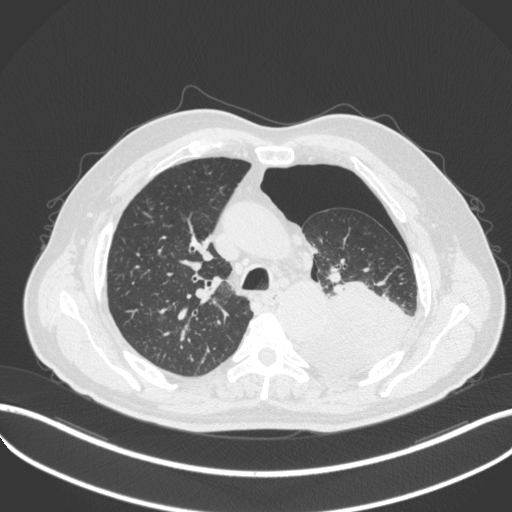
Chest CT, one axial slice. Position 357 of 466 along the scan axis. 120 kVp. Lung window (W 1500 / L -600 HU). 1 mm slice thickness. 512 × 512 image matrix, field of view 400 × 400 mm. Patient: male, 76 years. Case-level facts recorded for this patient, not image findings: clinical TNM (as recorded): T3 N0 M1b.
Annotated regions visible in this slice (rectangle marked by the reading radiologist):
- lung tumour (recorded histology: adenocarcinoma): bounding box [x1, y1, x2, y2] px = [290, 282, 417, 380]